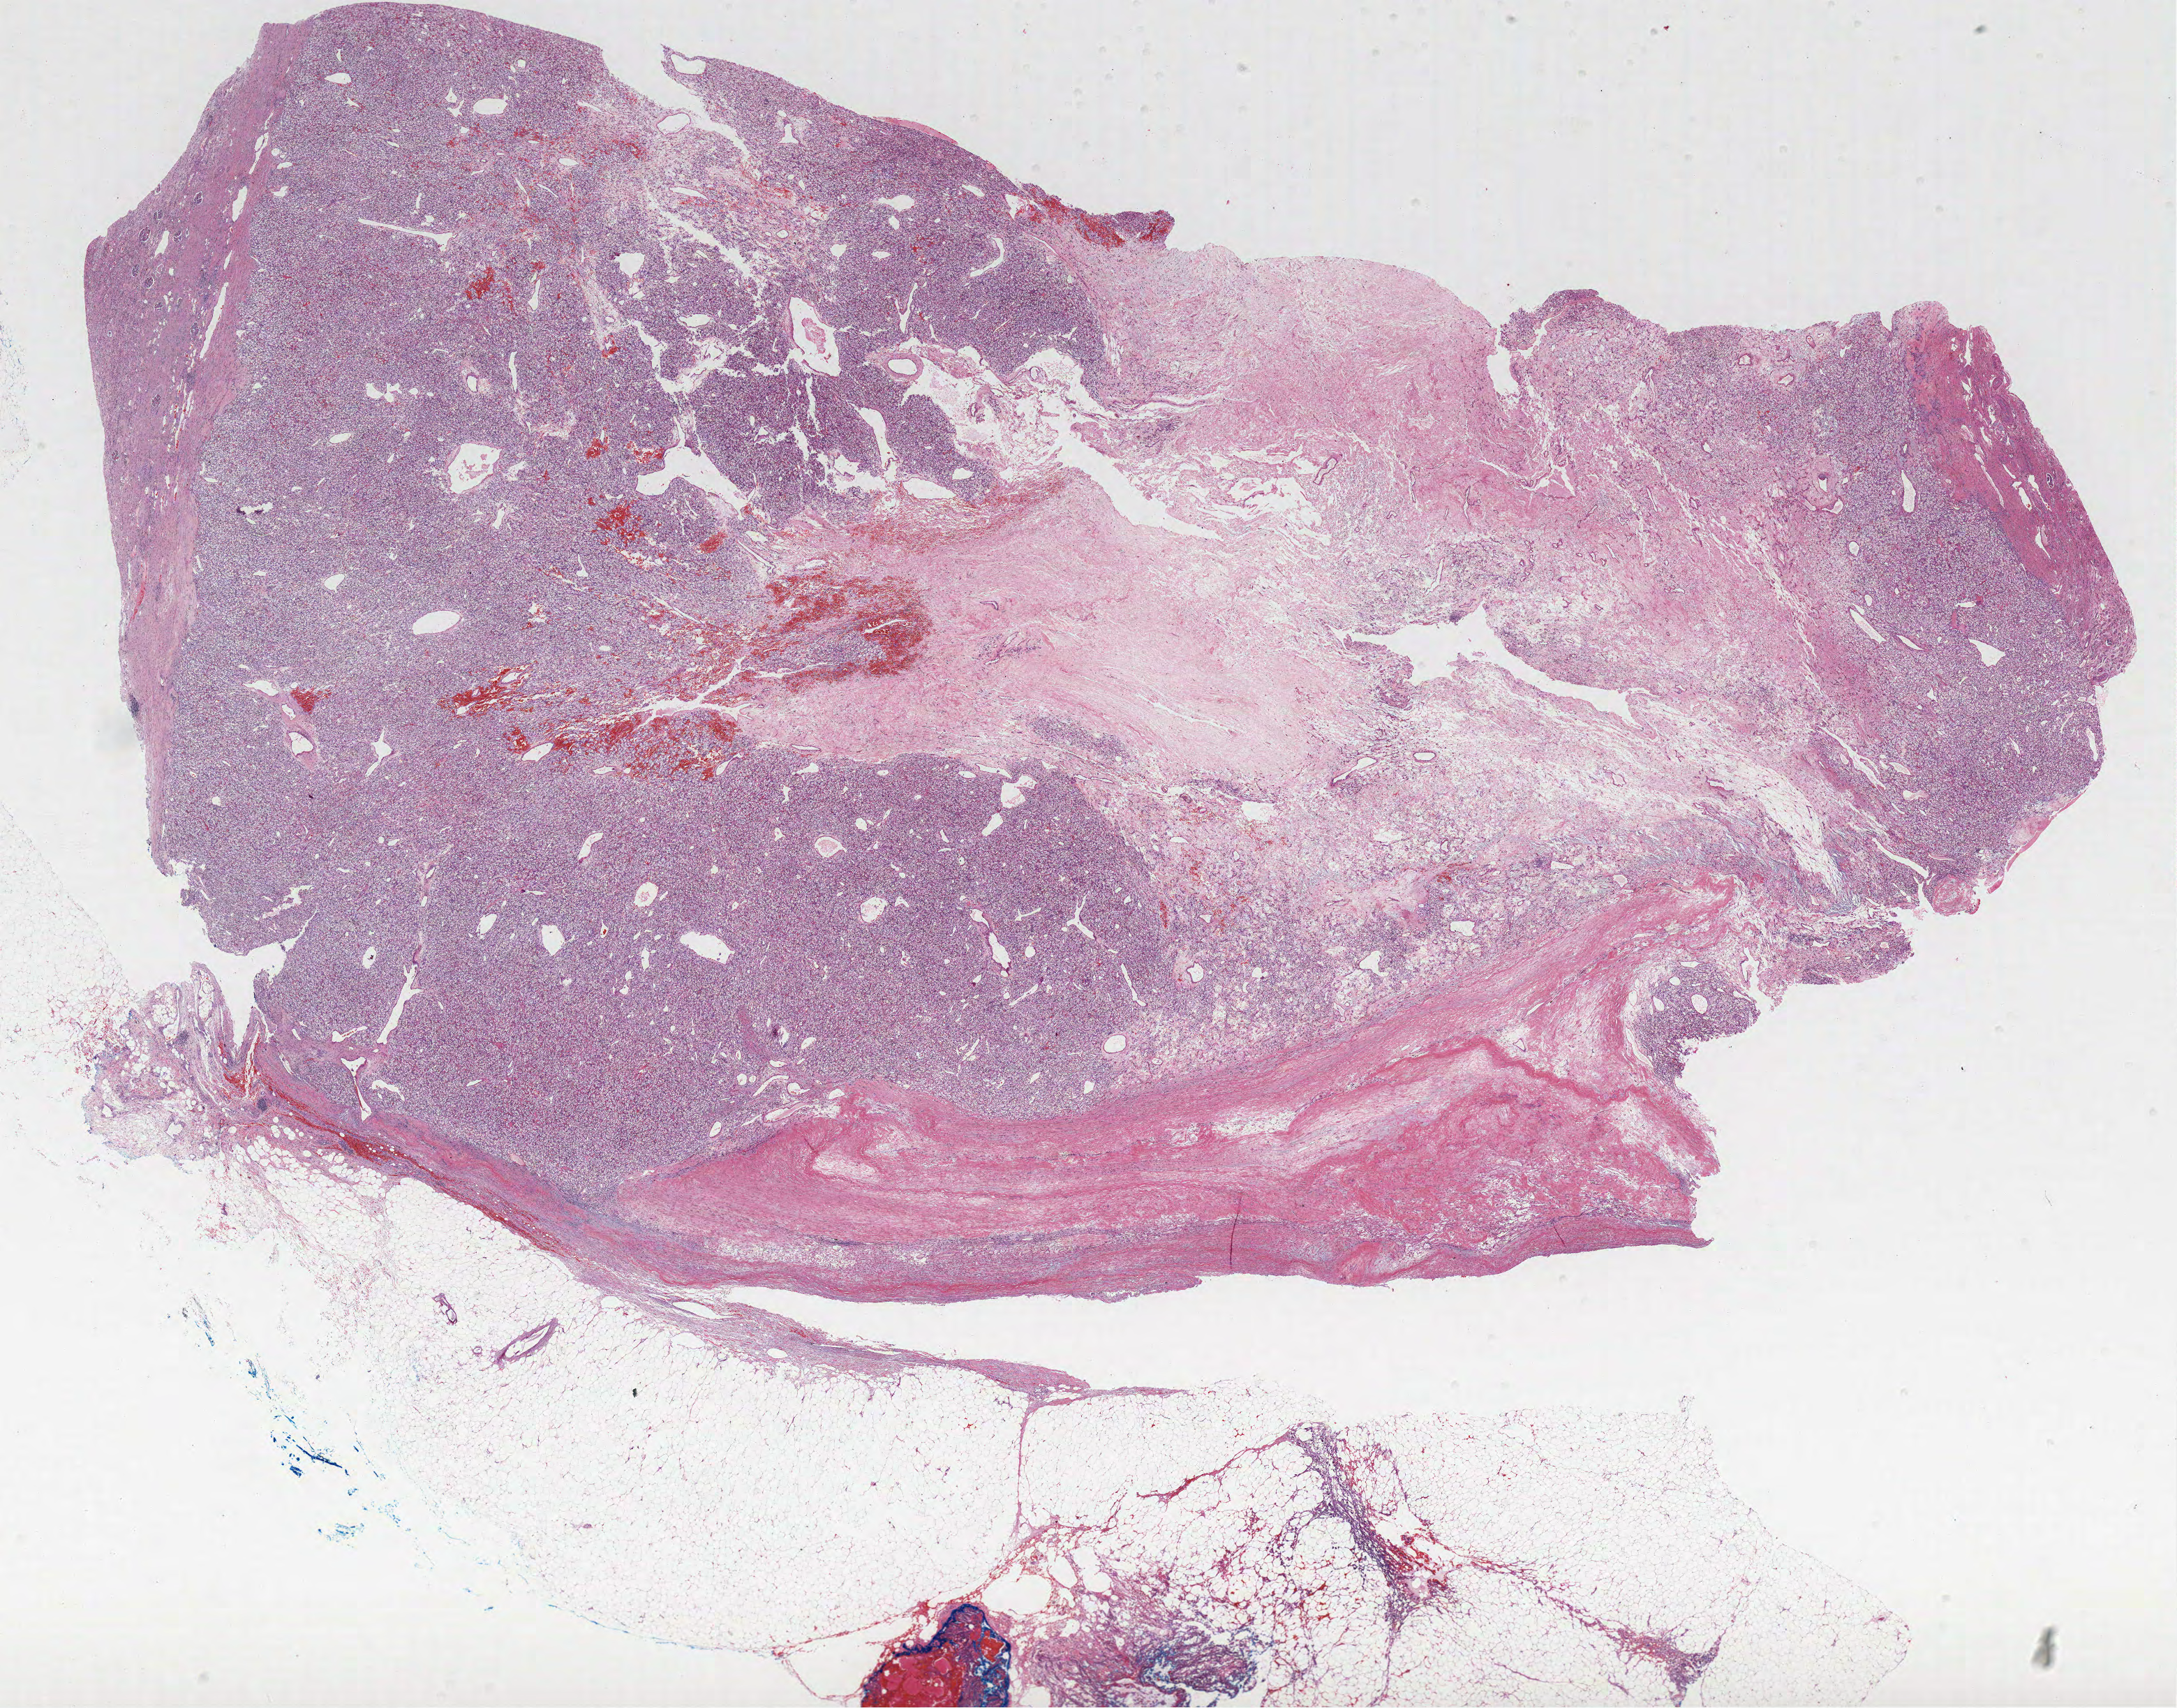
H&E whole-slide image — low-resolution overview of the scanned area, about 24.9 x 19.6 mm (slide scanned at 40x), formalin-fixed paraffin-embedded (FFPE) diagnostic section, primary tumour sample from the kidney. Patient: male, age at initial diagnosis 52 years. Histologic grade: G2 (moderately differentiated).
* TNM: T1a NX M0
* diagnosis: Clear cell adenocarcinoma, NOS
* AJCC pathologic stage: I